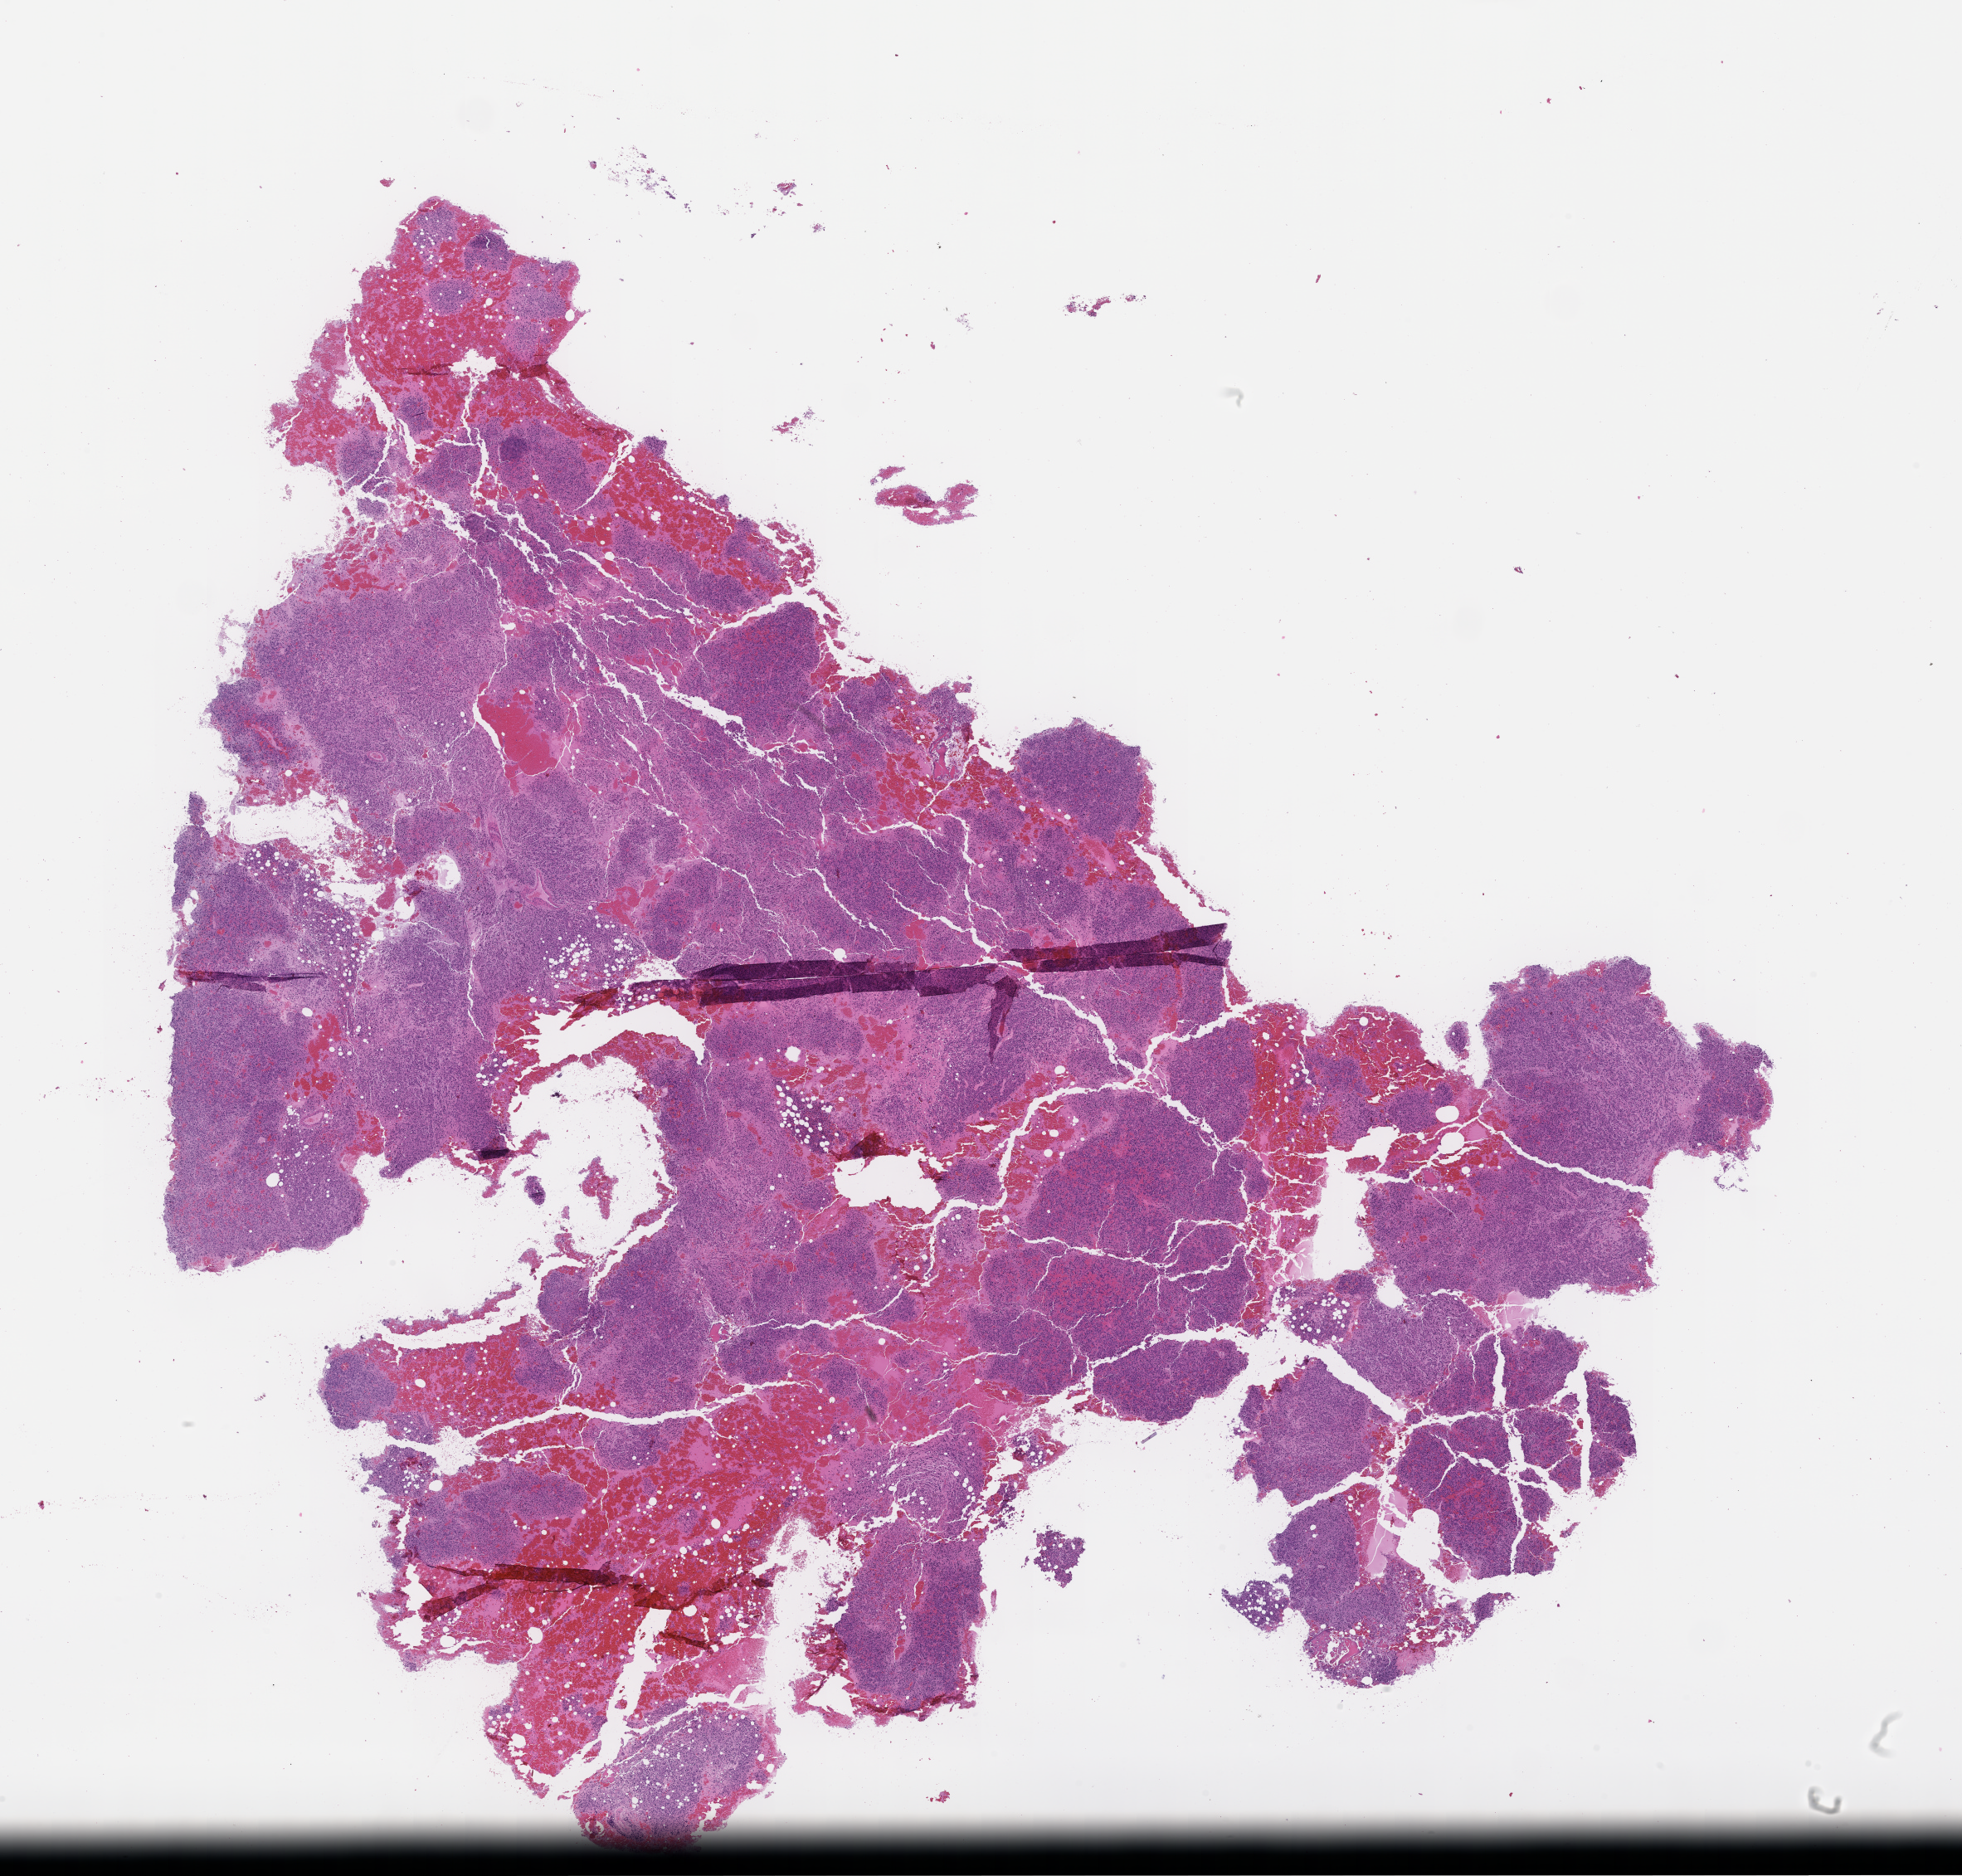
Whole-slide image, H&E stain — whole scanned area (about 19.1 x 18.3 mm) shown as a low-resolution overview; FFPE section; tissue site: bone marrow; archival tissue. Male patient.
This section: primary tumor. Diagnosis: Plasma Cell Myeloma.